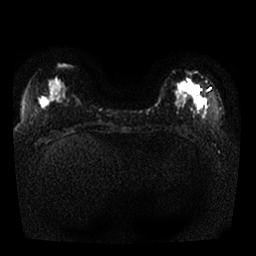
Breast MRI, one axial slice. Position 8 of 25 along the scan axis. Diffusion-weighted series; image 2 of 4 stored at this slice position (different b-values; order by instance number). 1.5 T. 4 mm slice thickness. 256 × 256 image matrix, field of view 330 × 330 mm. Female patient.
Annotated regions visible in this slice (expert manual segmentation):
- tumour on diffusion-weighted imaging: box from (x=179, y=83) to (x=198, y=92) px